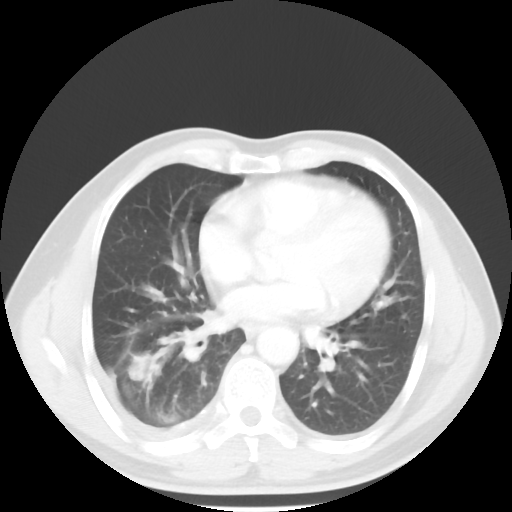
Chest CT, one axial slice; position 24 of 56 along the scan axis; lung window (W 1500 / L -600 HU); 5 mm slice thickness; 512 × 512 image matrix, field of view 344 × 344 mm. Patient: male, 56 years. Case-level facts recorded for this patient, not image findings: clinical TNM (as recorded): T2 N3 M1.
Outlined on this slice (rectangle marked by the reading radiologist):
- lung tumour (recorded histology: adenocarcinoma): bounding box (x1, y1, x2, y2) in pixels: (126, 351, 165, 389)